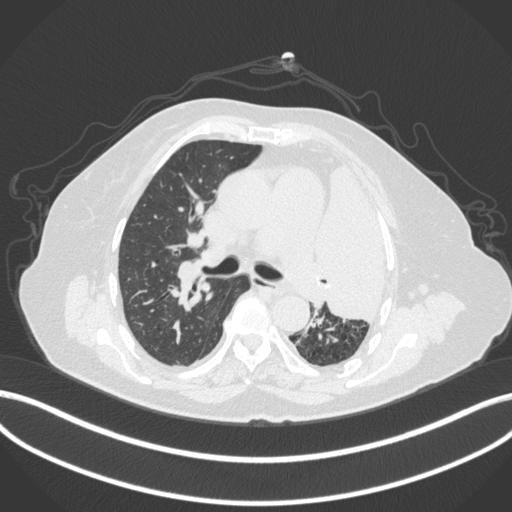
Chest CT, one axial slice; position 243 of 399 along the scan axis; reconstruction kernel B31f; 120 kVp; lung window (W 1500 / L -600 HU); 1 mm slice thickness; 512 × 512 image matrix, field of view 400 × 400 mm. Patient: female, 75 years. Case-level facts recorded for this patient, not image findings: clinical TNM (as recorded): T3 N3 M1.
Structures marked on this image (rectangle marked by the reading radiologist):
- lung tumour (recorded histology: adenocarcinoma): bounding box [x1, y1, x2, y2] px = [310, 167, 399, 326]